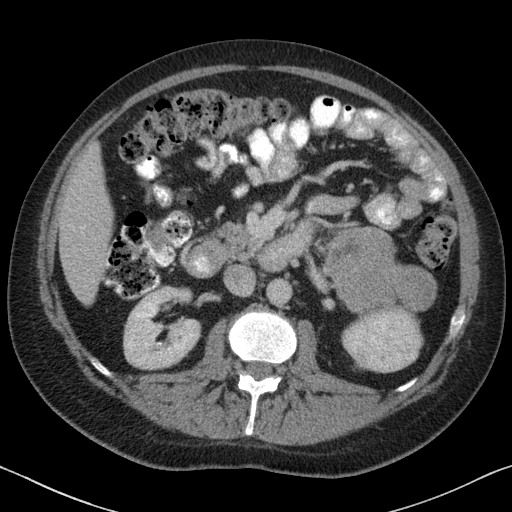
Contrast-enhanced abdominal CT, one axial slice. Slice 34 of 88 in the series (ordered by position). Reconstruction kernel B31f. 120 kVp. Intravenous contrast given. Soft-tissue window (W 400 / L 40 HU). 3 mm slice thickness. 512 × 512 image matrix, field of view 366 × 366 mm. Male patient, age 51 years. From the clinical record (not read from this slice): diagnosis: adrenocortical carcinoma; tumour side: left adrenal; tumour size at pathology: 16.5 cm; Ki-67 index: 30 %; stage (as recorded): 2.
Outlined on this slice (semi-automatically segmented with operator editing):
- mass: bounding box <326,230,436,312> (left, top, right, bottom; pixels)